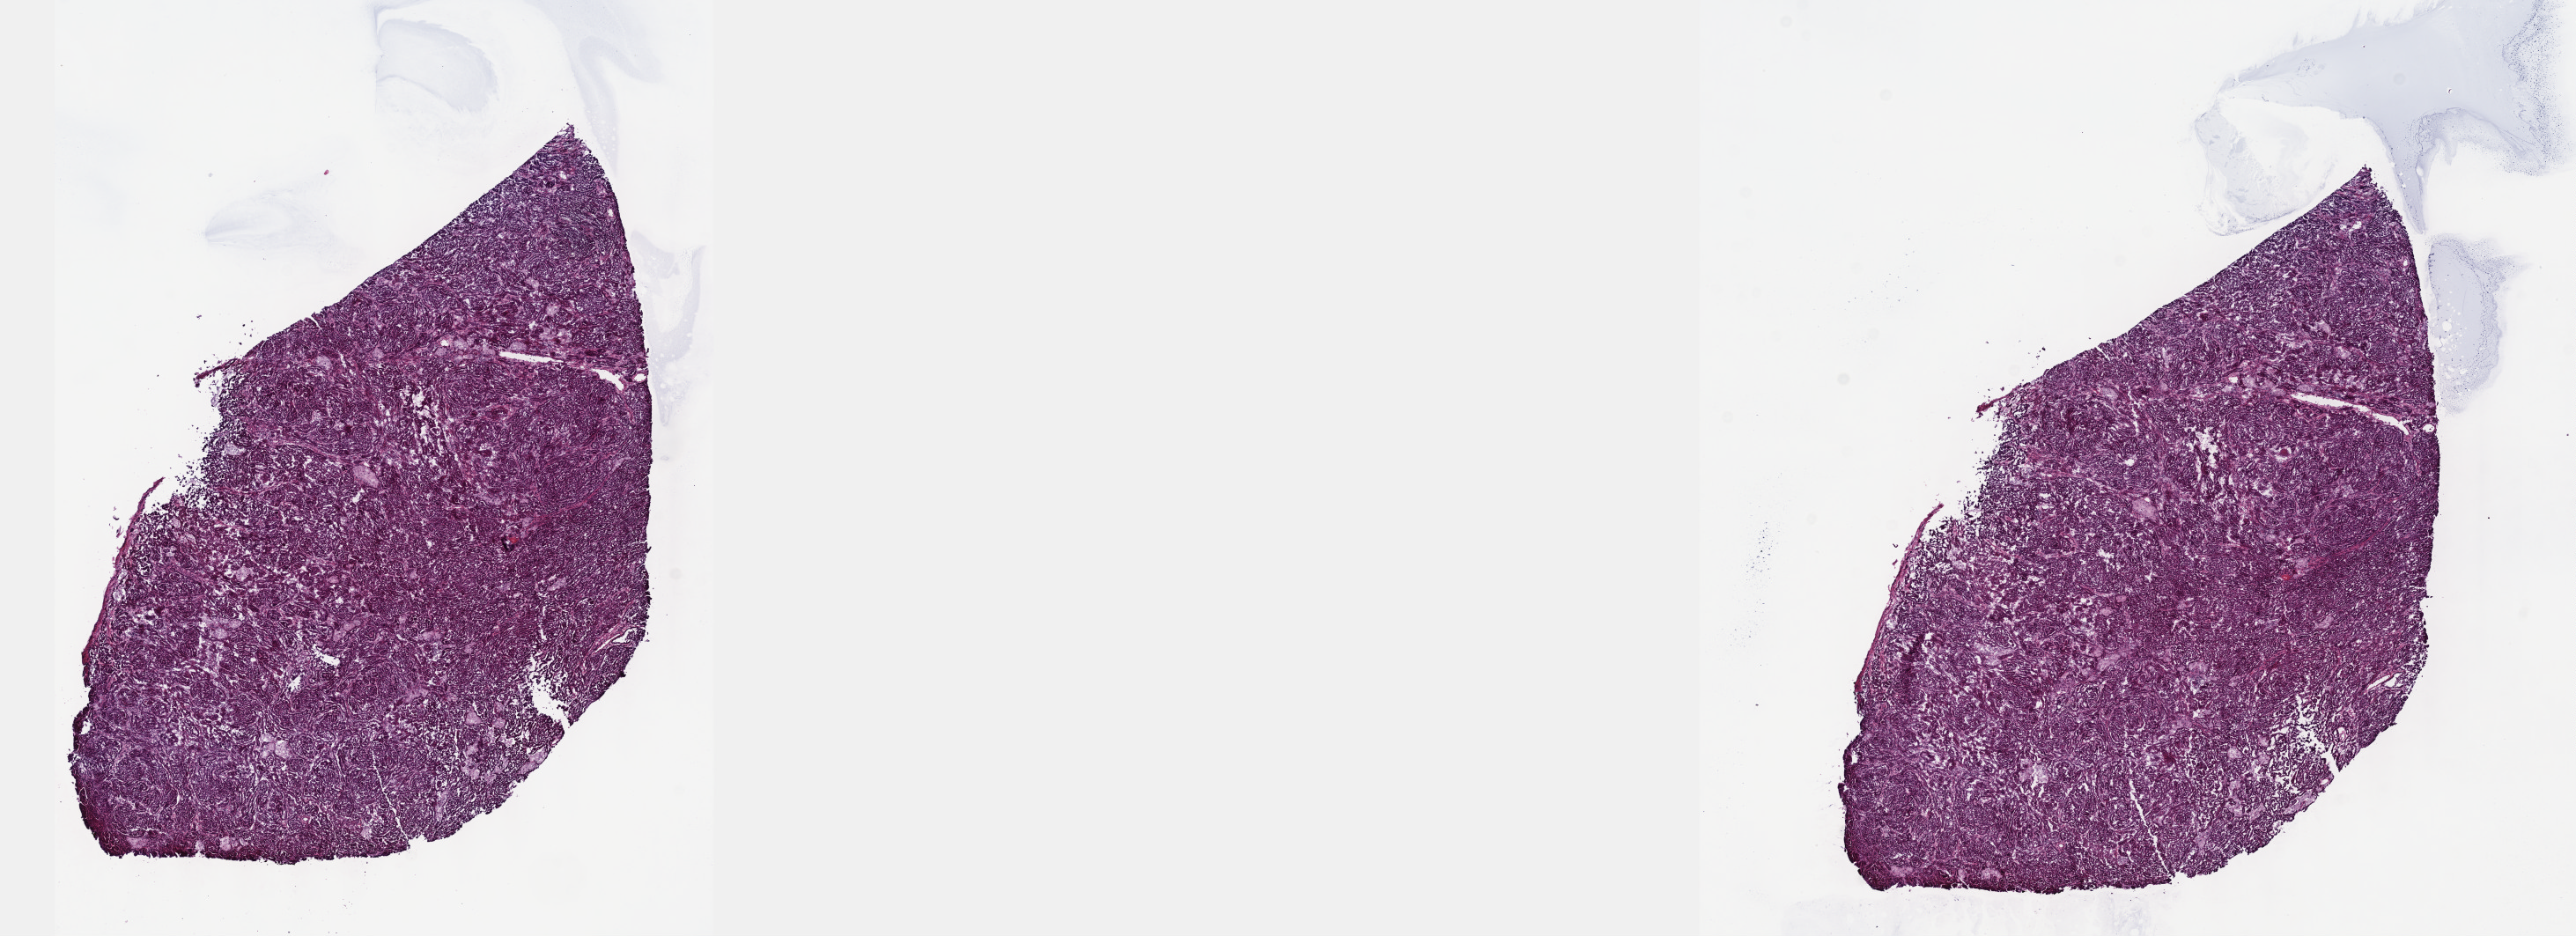
Digitized Hematoxylin and eosin (H&E) stained tissue section (whole slide), shown as a low-resolution overview of the whole scanned area (about 23.6 x 8.6 mm). Frozen section from the top of the tissue portion. Primary tumour sample from the kidney. Male patient; age at initial diagnosis 66 years. Pathologist review of this section (percent, as recorded): tumour cells 100%, tumour nuclei 80%, normal cells 0%, stromal cells 0%, necrosis 0%. Inflammatory infiltration, as recorded: lymphocyte infiltration 1%, monocyte infiltration 2%, neutrophil infiltration 0%.
* pathologic diagnosis: Papillary adenocarcinoma, NOS
* AJCC pathologic stage: I (7th edition)
* TNM: T1a NX MX